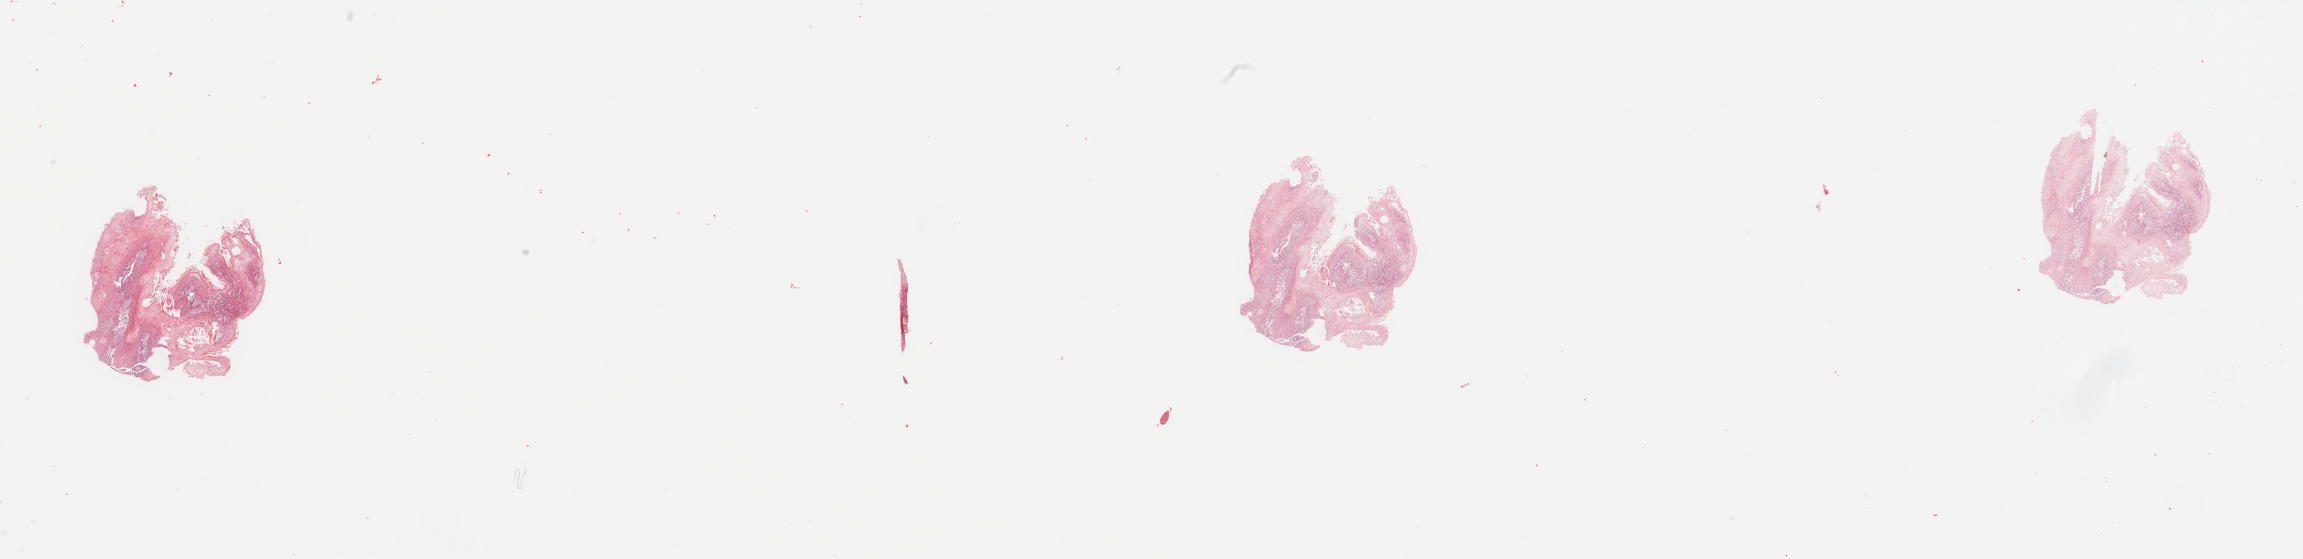
Whole-slide histology image, Hematoxylin and eosin (H&E) stained, whole scanned area (about 36.4 x 8.8 mm, slide scanned at 20x) shown as a low-resolution overview. Tumour tissue sample, sampled site: floor of mouth. Male, 45 y/o. Histologic grade: G1 (well differentiated). Slide review estimates, as recorded: tumour nuclei 85%, necrosis 5%.
• AJCC pathologic stage: III
• diagnosis: Squamous cell carcinoma, NOS (floor of mouth, NOS)